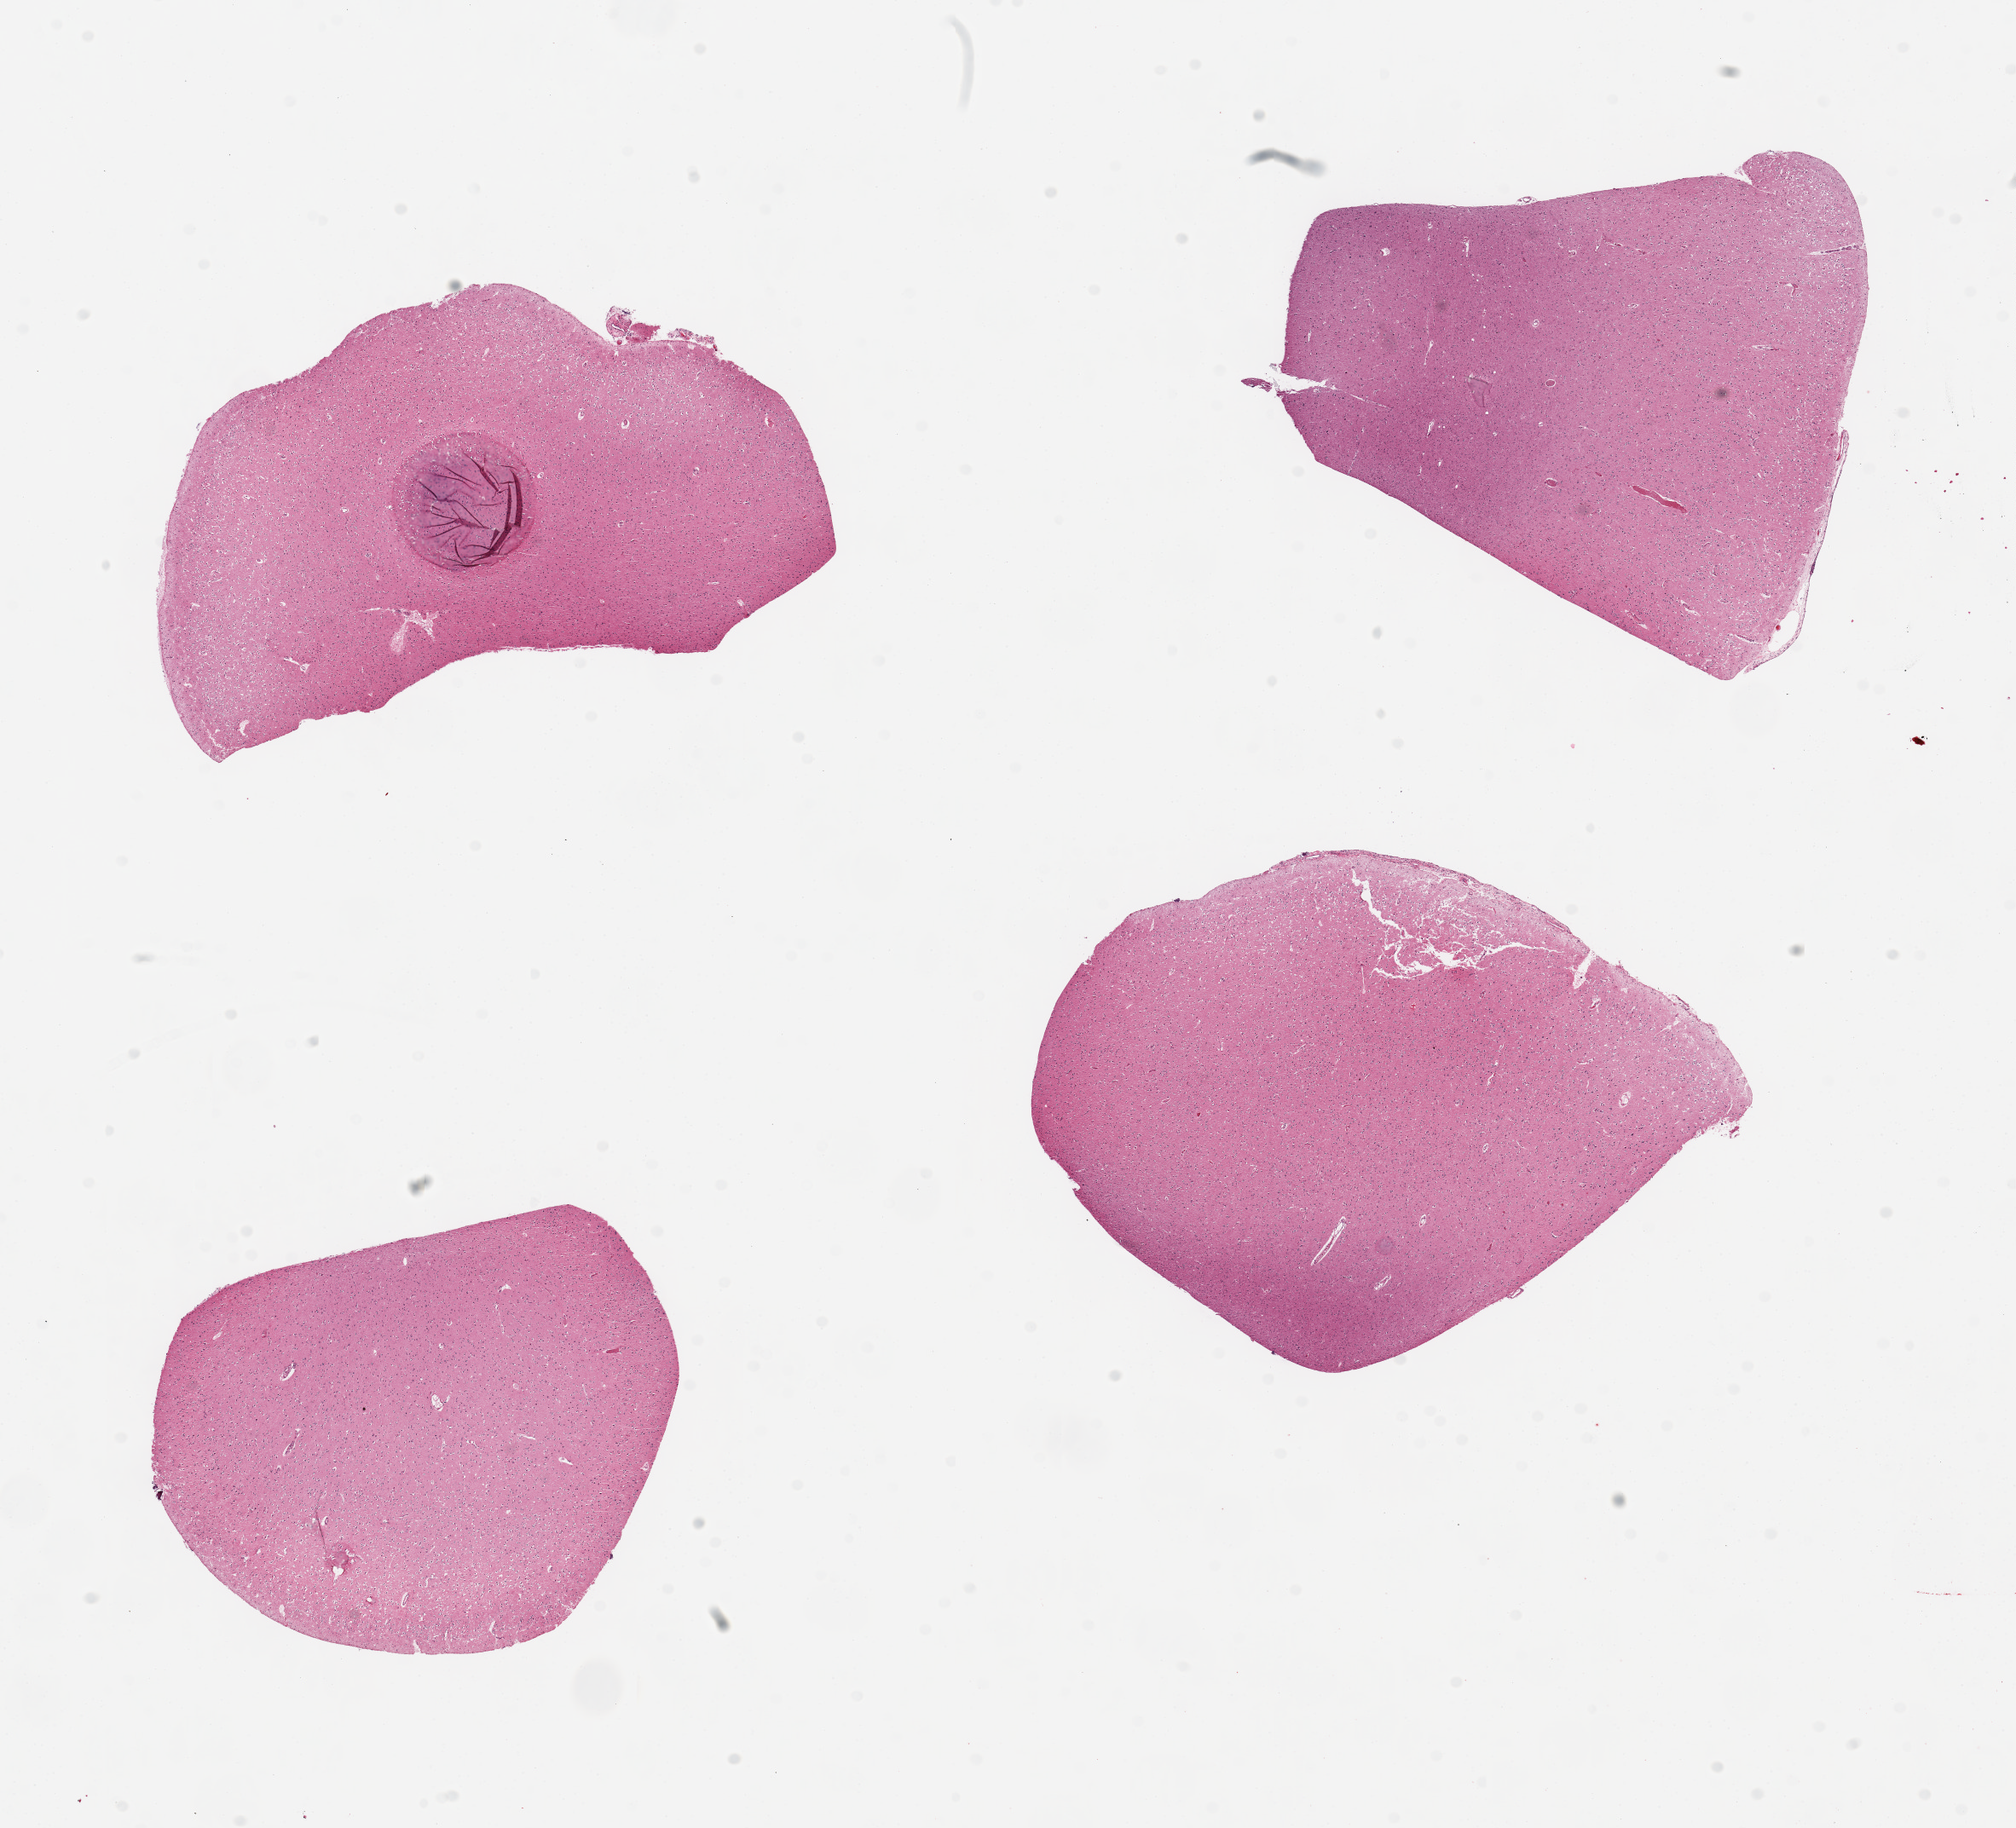
Digitized haematoxylin and eosin-stained section, a low-resolution overview of the entire scanned area, about 18.7 x 17.0 mm; PAXgene-fixed paraffin-embedded (PFPE) section; target tissue: cerebral cortex; tissue donor sample. Donor sex: male.
Pathologist's review note for this sample: 1 aliquot pituitary, ~5x3mm. All neurohypophysis.